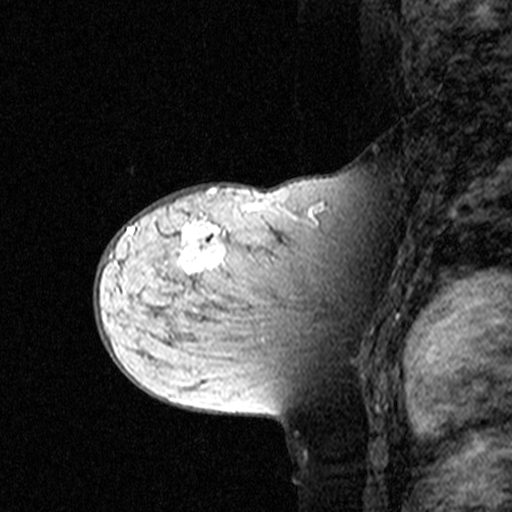
Breast MRI (dynamic contrast-enhanced), one sagittal slice; position 25 of 44 along the scan axis; dynamic contrast-enhanced study with each time point stored as its own series, time point 2 of 3 at this slice position (early post-contrast, ordered by acquisition time); 1.5 T; TE 4.5 ms, TR 11 ms; 3 mm slice thickness; 512 × 512 image matrix. Patient: female, 44 years. From the clinical record (not read from this slice): setting: breast cancer imaged before/during neoadjuvant chemotherapy; receptor status: triple-negative.
Structures marked on this image (semi-automatically segmented with operator editing):
- analysis volume of interest (the breast-tissue region the enhancement analysis was run in; not a lesion): bounding box [x1, y1, x2, y2] px = [142, 208, 349, 363]
- tumour enhancement mask (voxels above the 90 % enhancement threshold inside the analysis volume of interest): [181, 212, 314, 272]